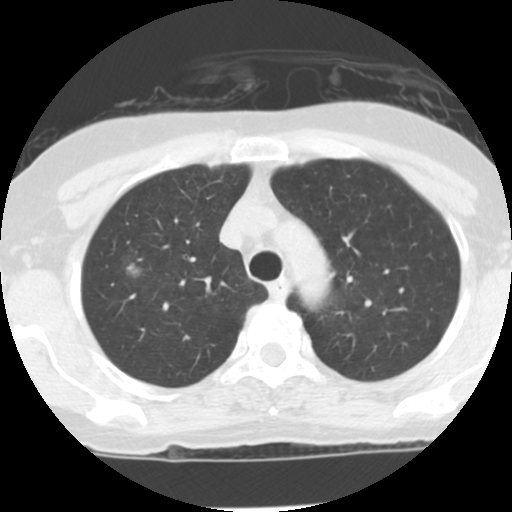
Low-dose screening chest CT, one axial slice. Position 97 of 122 along the scan axis. Reconstruction kernel STANDARD. Lung window (W 1500 / L -600 HU). 2.5 mm slice thickness. 512 × 512 image matrix, field of view 290 × 290 mm.
Structures marked on this image (expert manual segmentation):
- lesion 1 (tumor, upper lobe of right lung): bounding box [x1, y1, x2, y2] px = [126, 262, 140, 275]